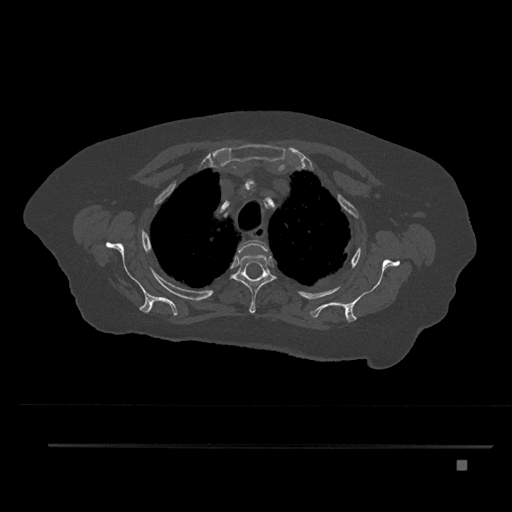
CT including the spine, one axial slice. Position 639 of 797 along the scan axis. Reconstruction kernel Br40s/3. 120 kVp. Bone window (W 1800 / L 400 HU). 512 × 512 image matrix, field of view 437 × 437 mm. Patient: female, 76 years. From the clinical record (not read from this slice): primary cancer: lung; vertebrae with lytic lesions (as recorded): T11, L3.
Structures marked on this image (semi-automatically segmented with operator editing):
- T2 vertebra: bounding box [x1, y1, x2, y2] px = [237, 240, 268, 256]
- T3 vertebra: [230, 254, 277, 314]